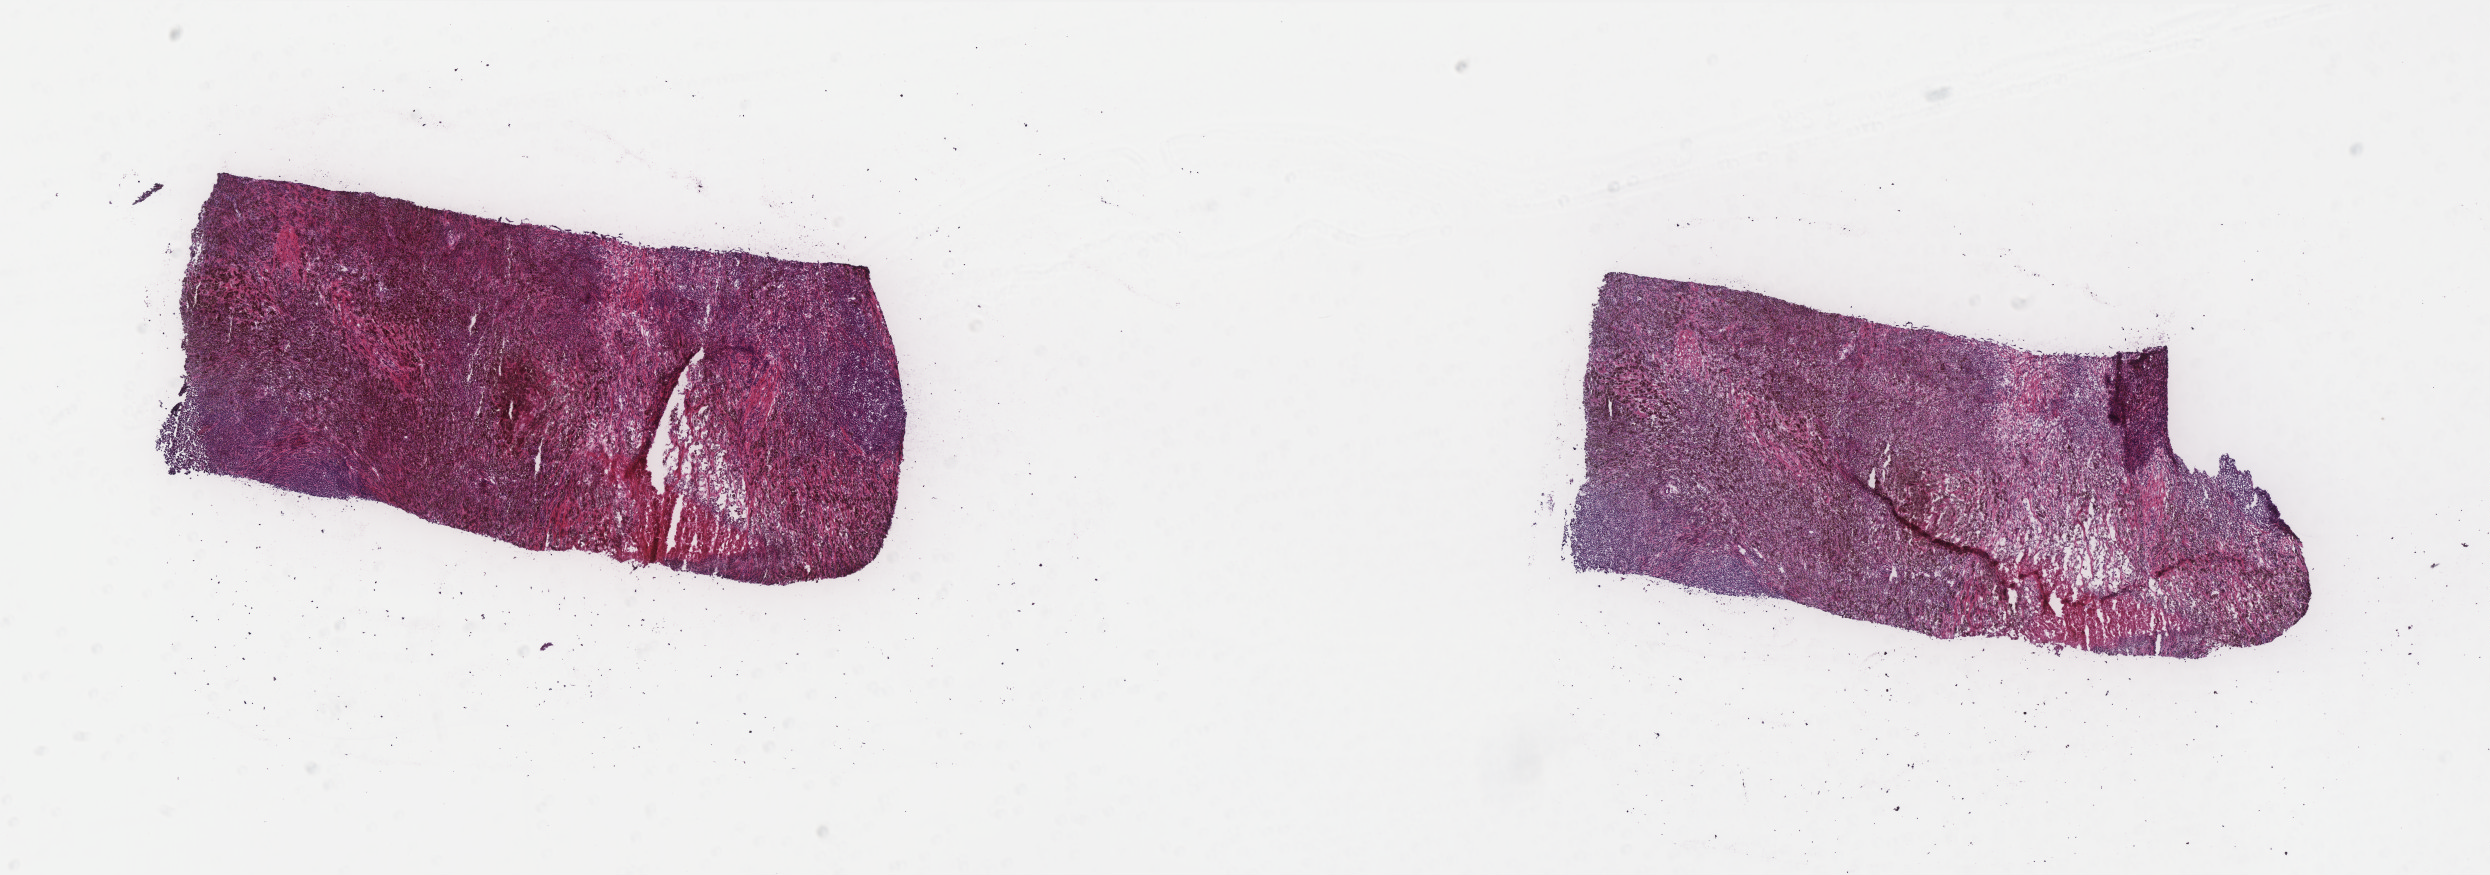
H&E-stained whole-slide image — a low-resolution overview of the entire scanned area, about 20.0 x 7.0 mm (from a 40x scan). Frozen section from the top of the tissue portion. Metastatic tumour sample, sampled site: connective, subcutaneous and other soft tissues of thorax. Male, age 47 years at initial diagnosis. Pathologist review of this section (percent, as recorded): tumour cells 75%, tumour nuclei 70%, normal cells 0%, stromal cells 15%, necrosis 10%. Inflammatory infiltration, as recorded: lymphocyte infiltration 0%, monocyte infiltration 0%, neutrophil infiltration 0%.
- this section: metastatic tumour tissue
- patient diagnosis: Malignant melanoma, NOS